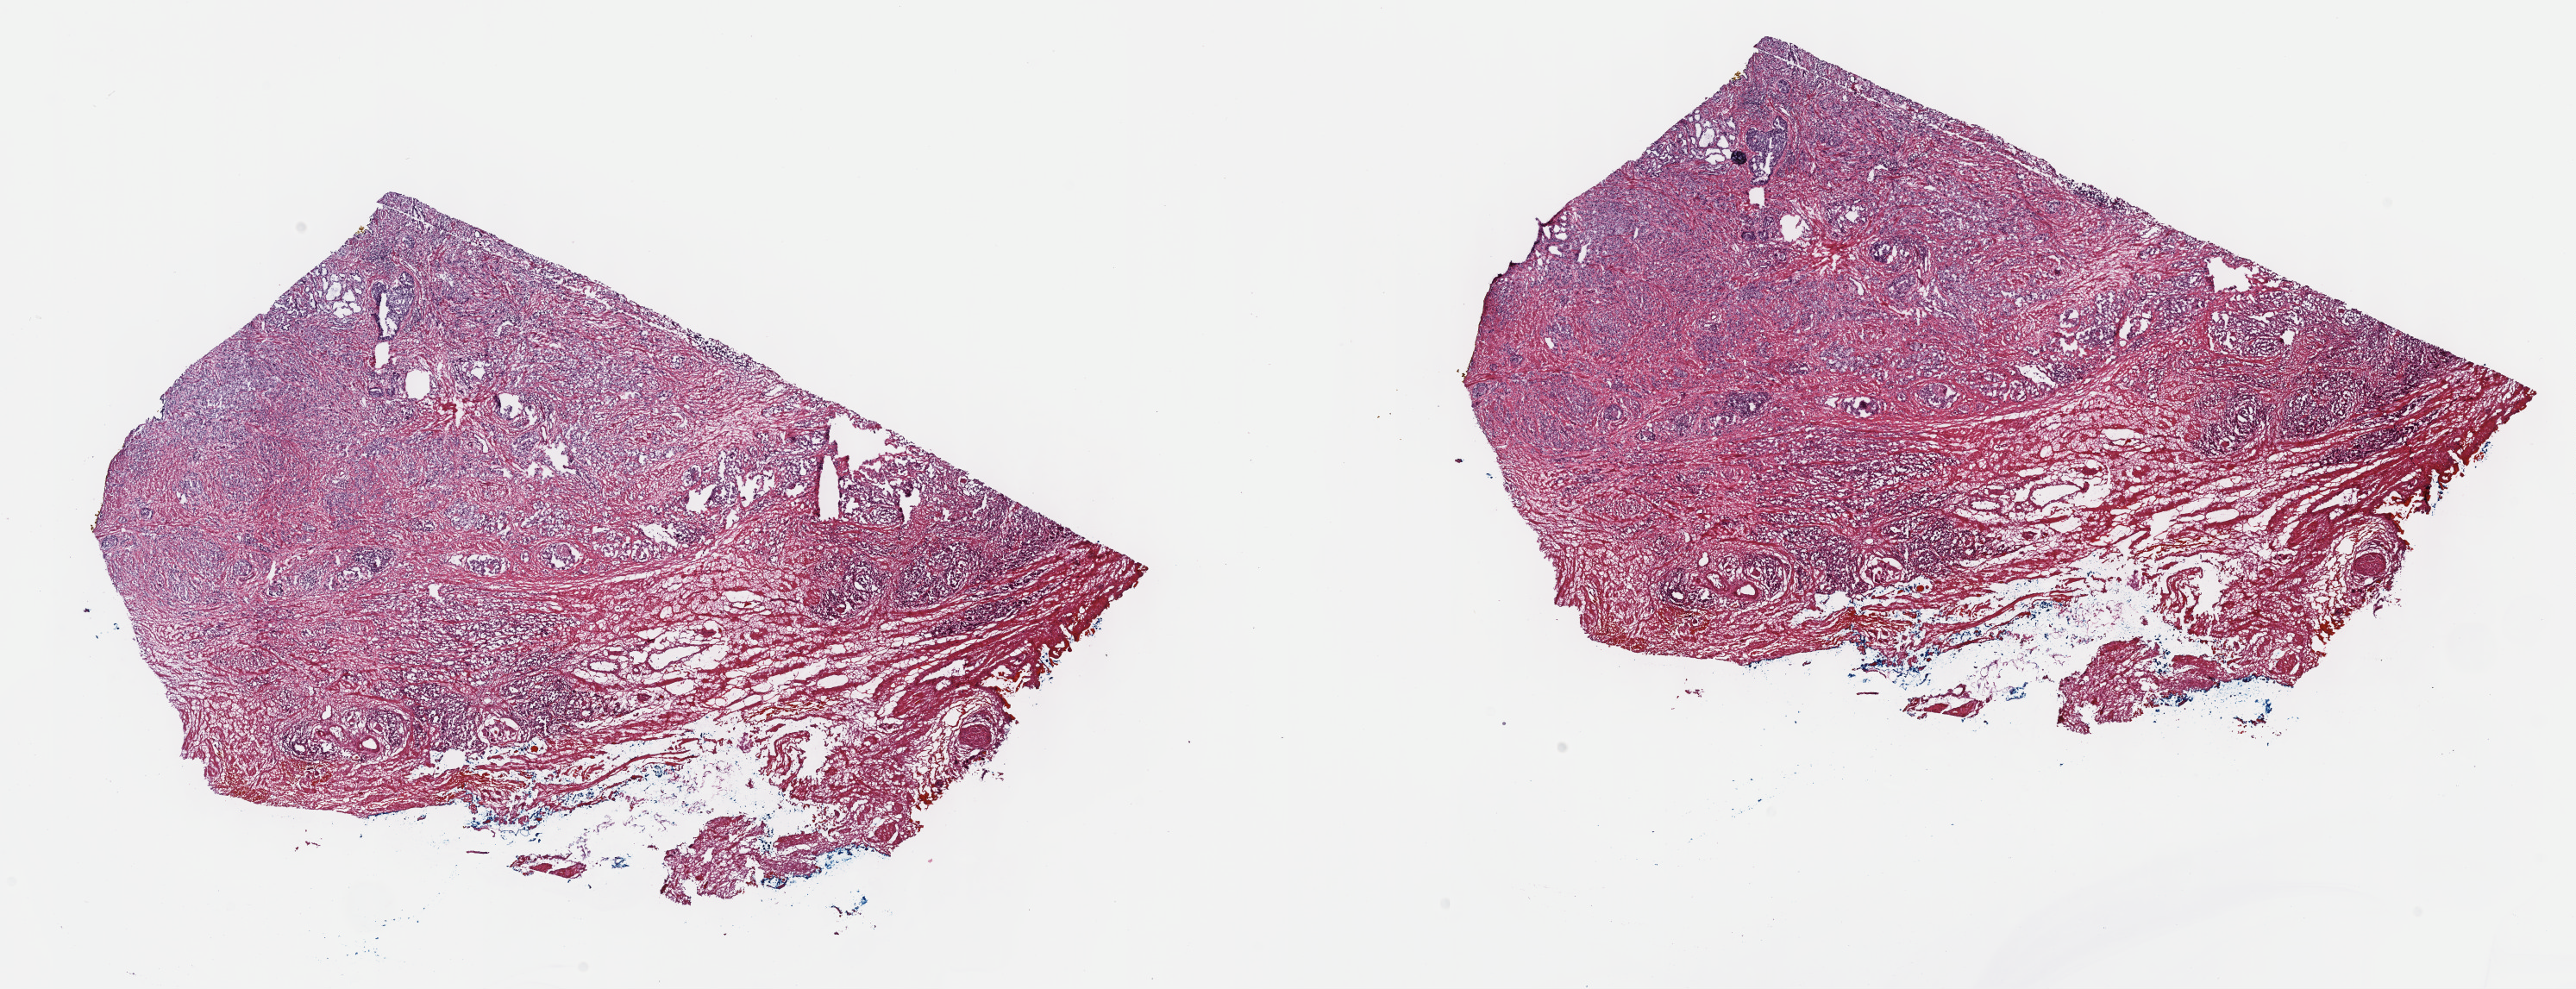
H&E whole-slide image — a low-resolution overview of the entire scanned area, about 24.2 x 9.3 mm, frozen section from the top of the tissue portion, primary tumour sample from the prostate. Patient: male, age at initial diagnosis 64 years. Pathologist review of this section (percent, as recorded): tumour cells 100%, tumour nuclei 65%.
Histologic diagnosis: Adenocarcinoma, NOS (prostate gland).